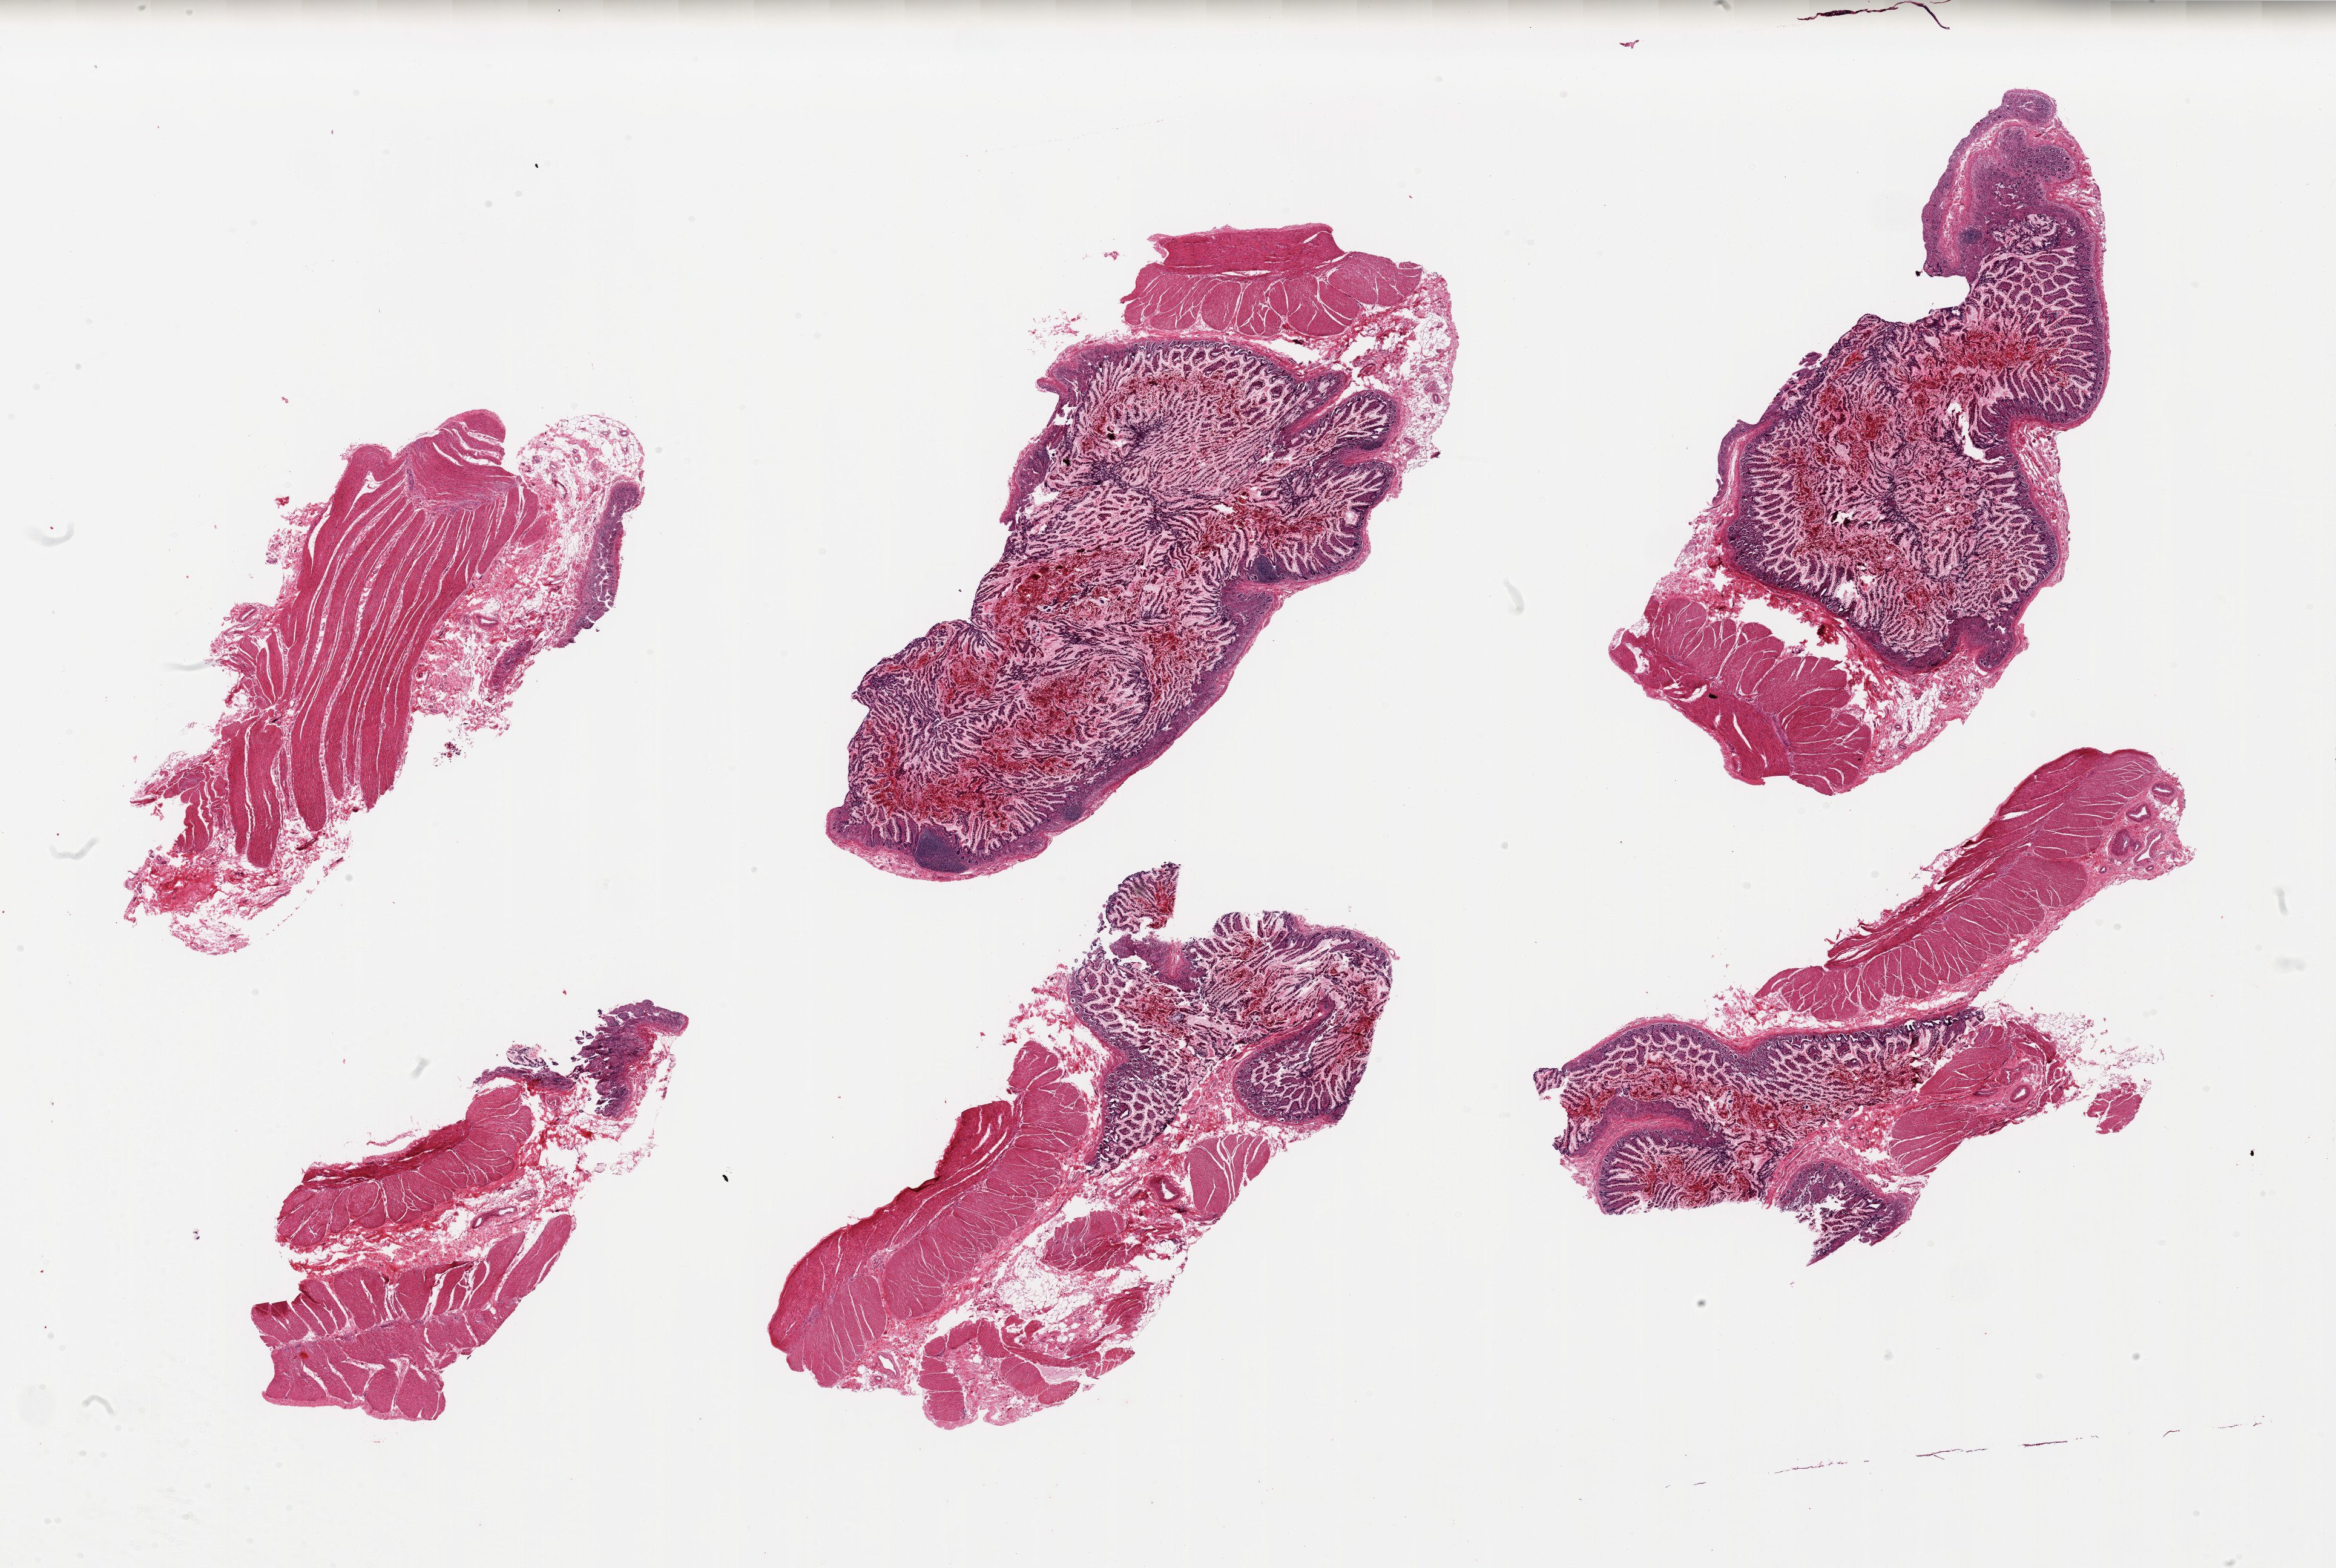
Digitized H&E-stained section, low-resolution overview of the scanned area, about 30.5 x 20.5 mm. PAXgene-fixed, paraffin-embedded tissue. Section of ileum (target tissue). Donor tissue sample. Donor sex: male.
Reviewer comment on this tissue sample: 6 pieces, mucosa/muscularis, less than 5% lymphoid aggregates.